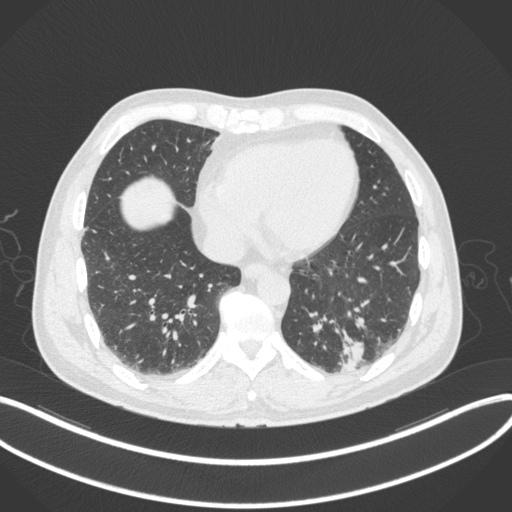
Chest CT, one axial slice; slice 88 of 313 in the series (ordered by position); reconstruction kernel B31f; 120 kVp; lung window (W 1500 / L -600 HU); 1 mm slice thickness; 512 × 512 image matrix, field of view 400 × 400 mm. Male patient, age 54 years. From the clinical record (not read from this slice): clinical TNM (as recorded): T1c N0 M1.
Outlined on this slice (bounding box drawn by a radiologist):
- lung tumour (recorded histology: adenocarcinoma): bounding box [x1, y1, x2, y2] px = [332, 329, 368, 379]